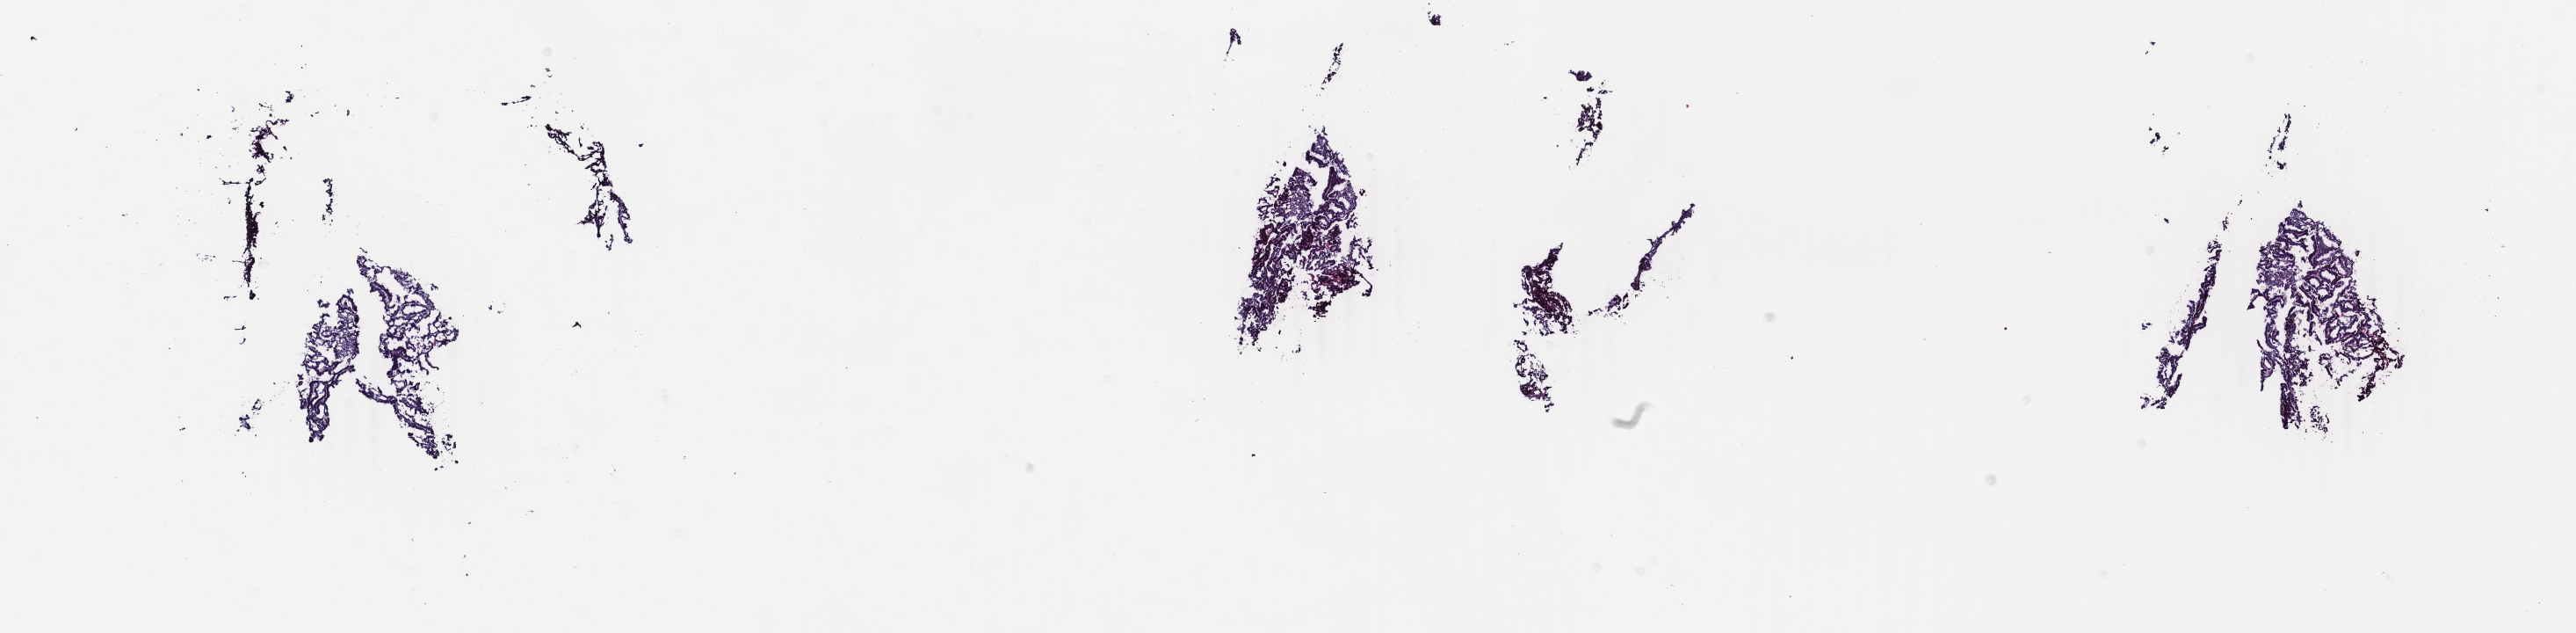
H&E whole-slide image — whole scanned area (about 23.3 x 5.7 mm, from a 40x scan) shown as a low-resolution overview; frozen section from the top of the tissue portion; primary tumour sample from the uterus. Female patient; age at initial diagnosis 63 years.
Pathologic diagnosis: Endometrioid adenocarcinoma, NOS (endometrium).